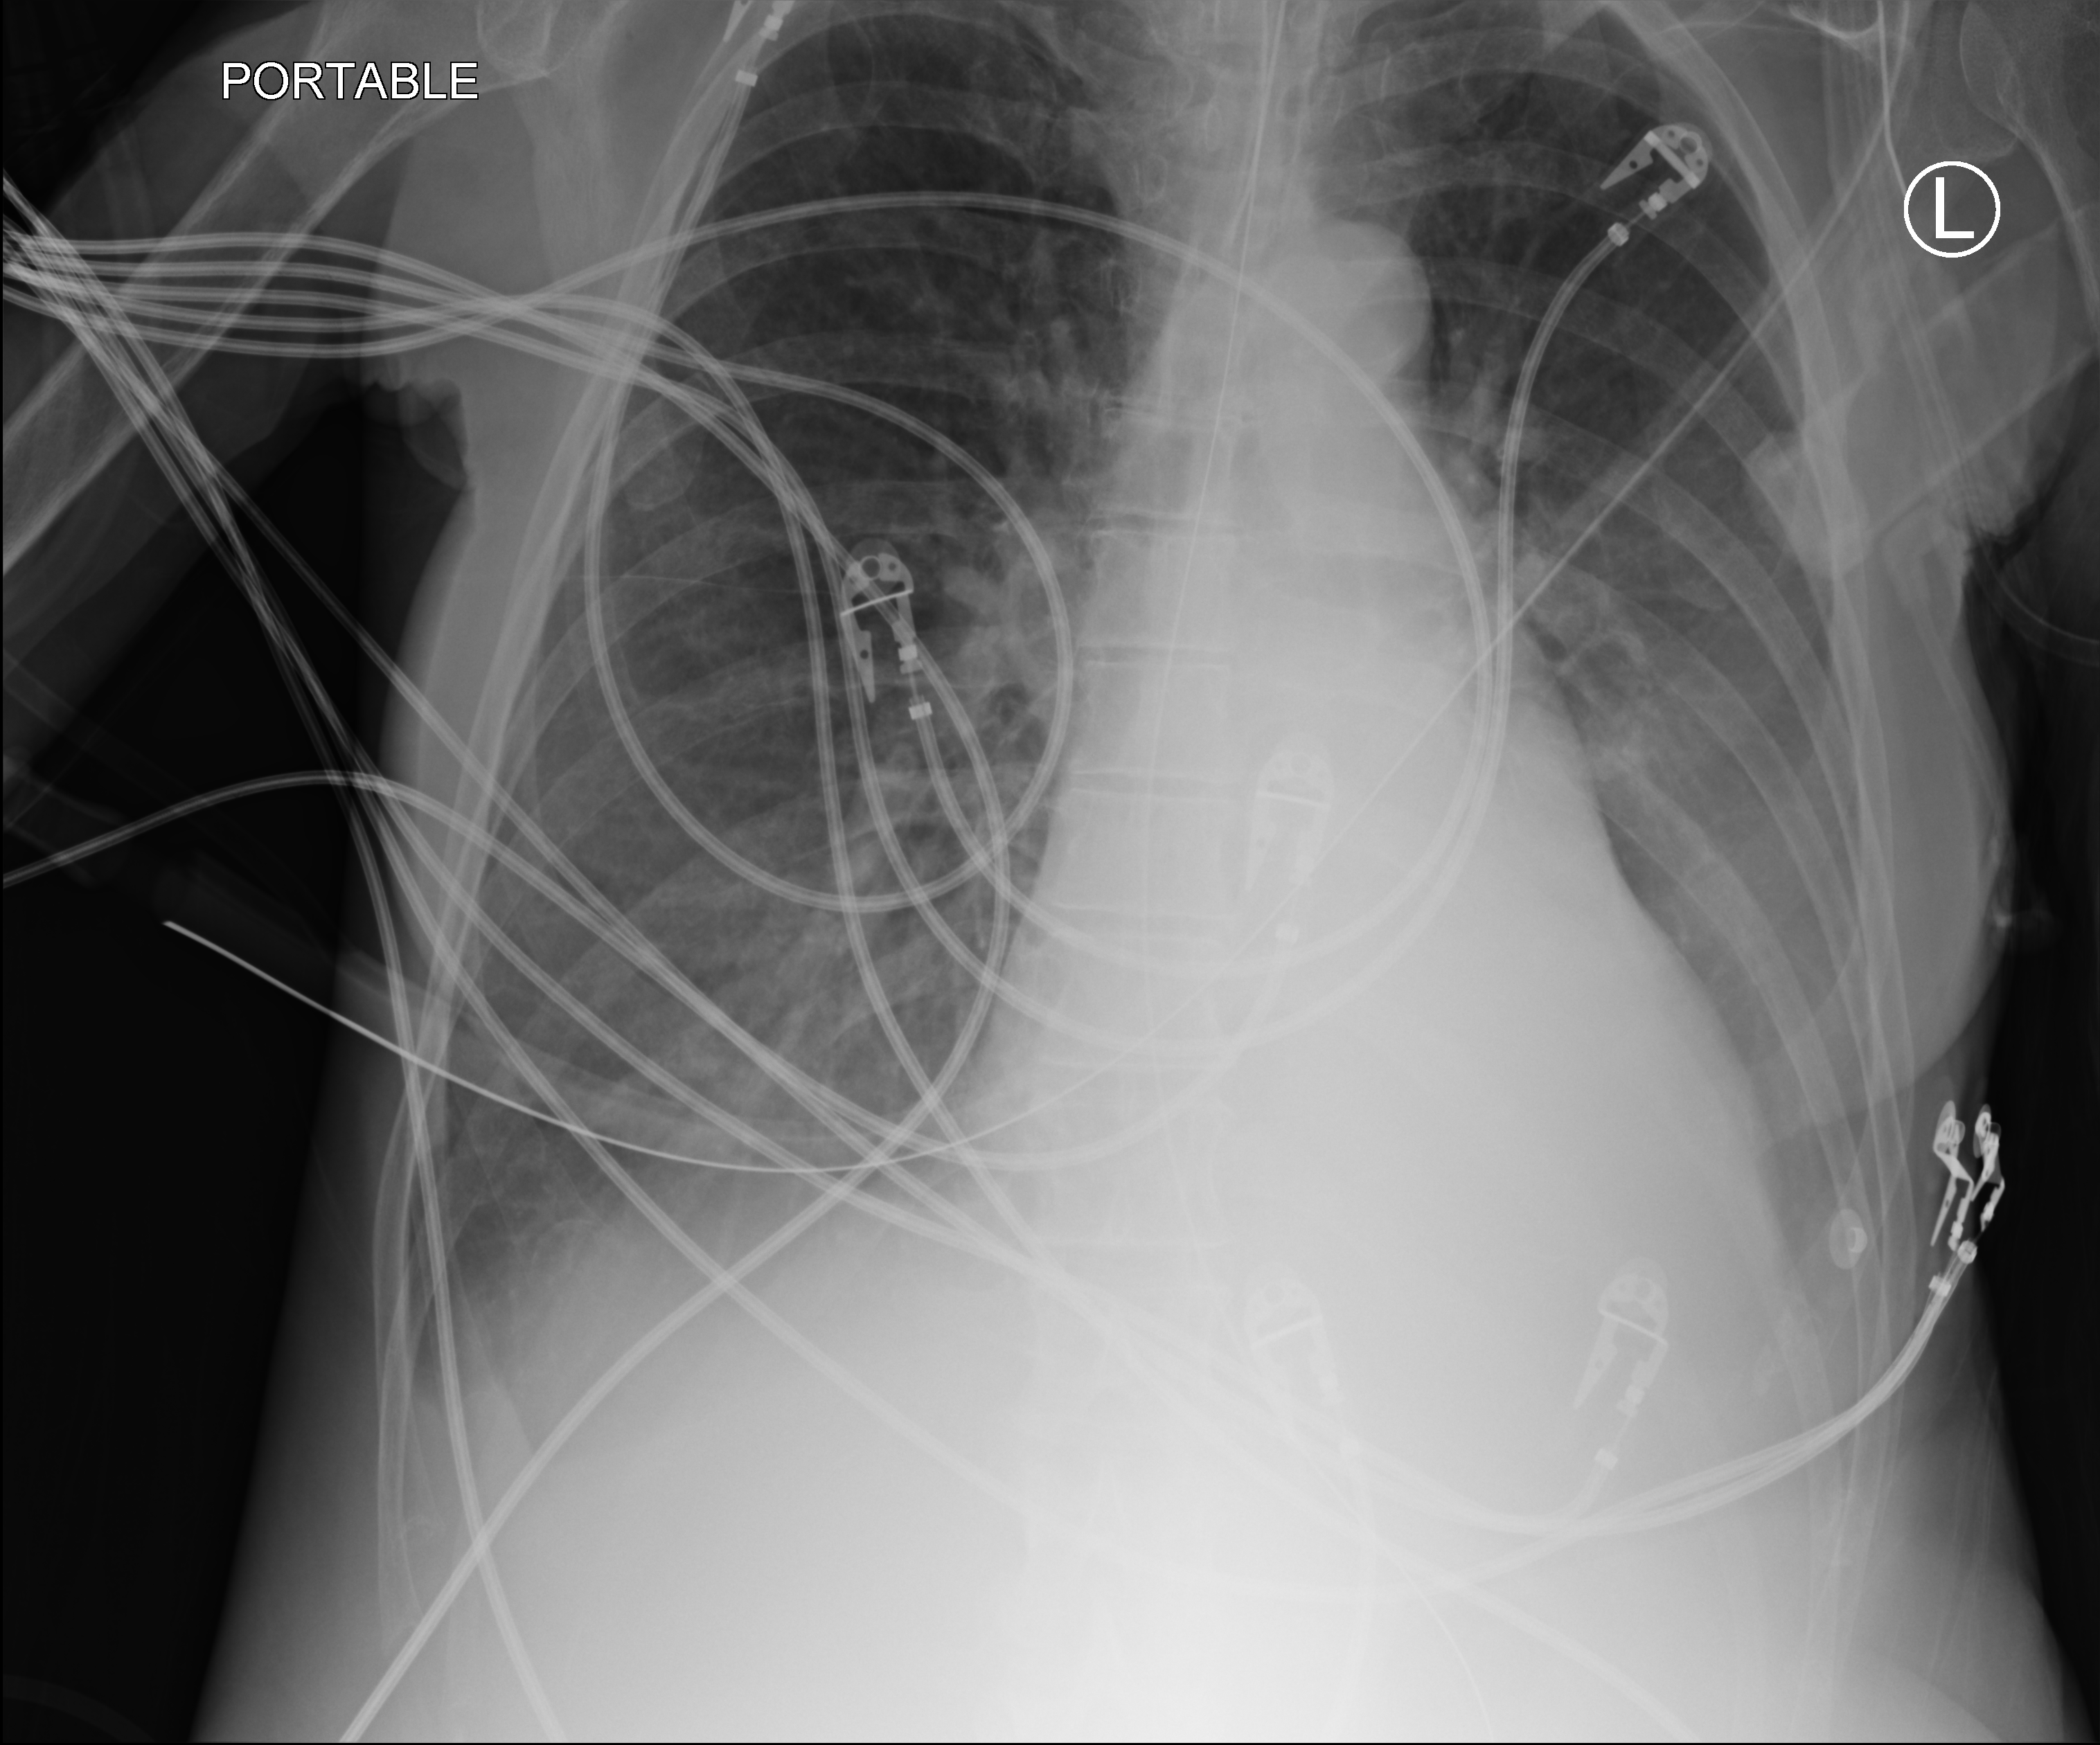
Chest X-ray (portable). Female patient hospitalised with COVID-19, age 60–74 years.
From the hospital-stay record, not from the radiograph (when in the stay this image was taken is not recorded):
- admitted to intensive care during this hospital stay: yes
- mechanically ventilated during this hospital stay: yes